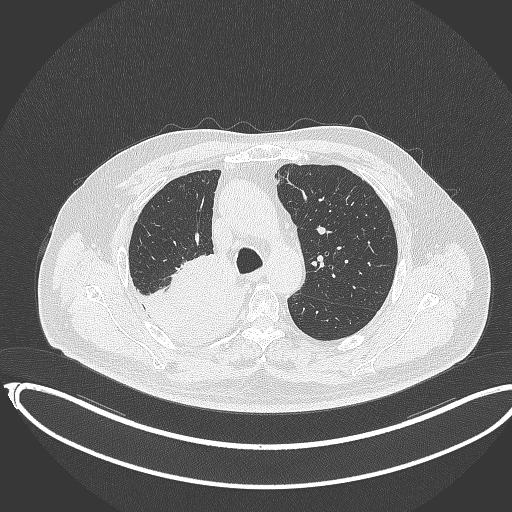
Chest CT, one axial slice. Position 256 of 403 along the scan axis. 120 kVp. Lung window (W 1500 / L -600 HU). 1 mm slice thickness. 512 × 512 image matrix, field of view 436 × 436 mm. Male patient, age 68 years. Case-level facts recorded for this patient, not image findings: clinical TNM (as recorded): T2a N0 M0.
Annotated regions visible in this slice (bounding box drawn by a radiologist):
- lung tumour (recorded histology: adenocarcinoma): bounding box [x1, y1, x2, y2] px = [131, 254, 243, 338]